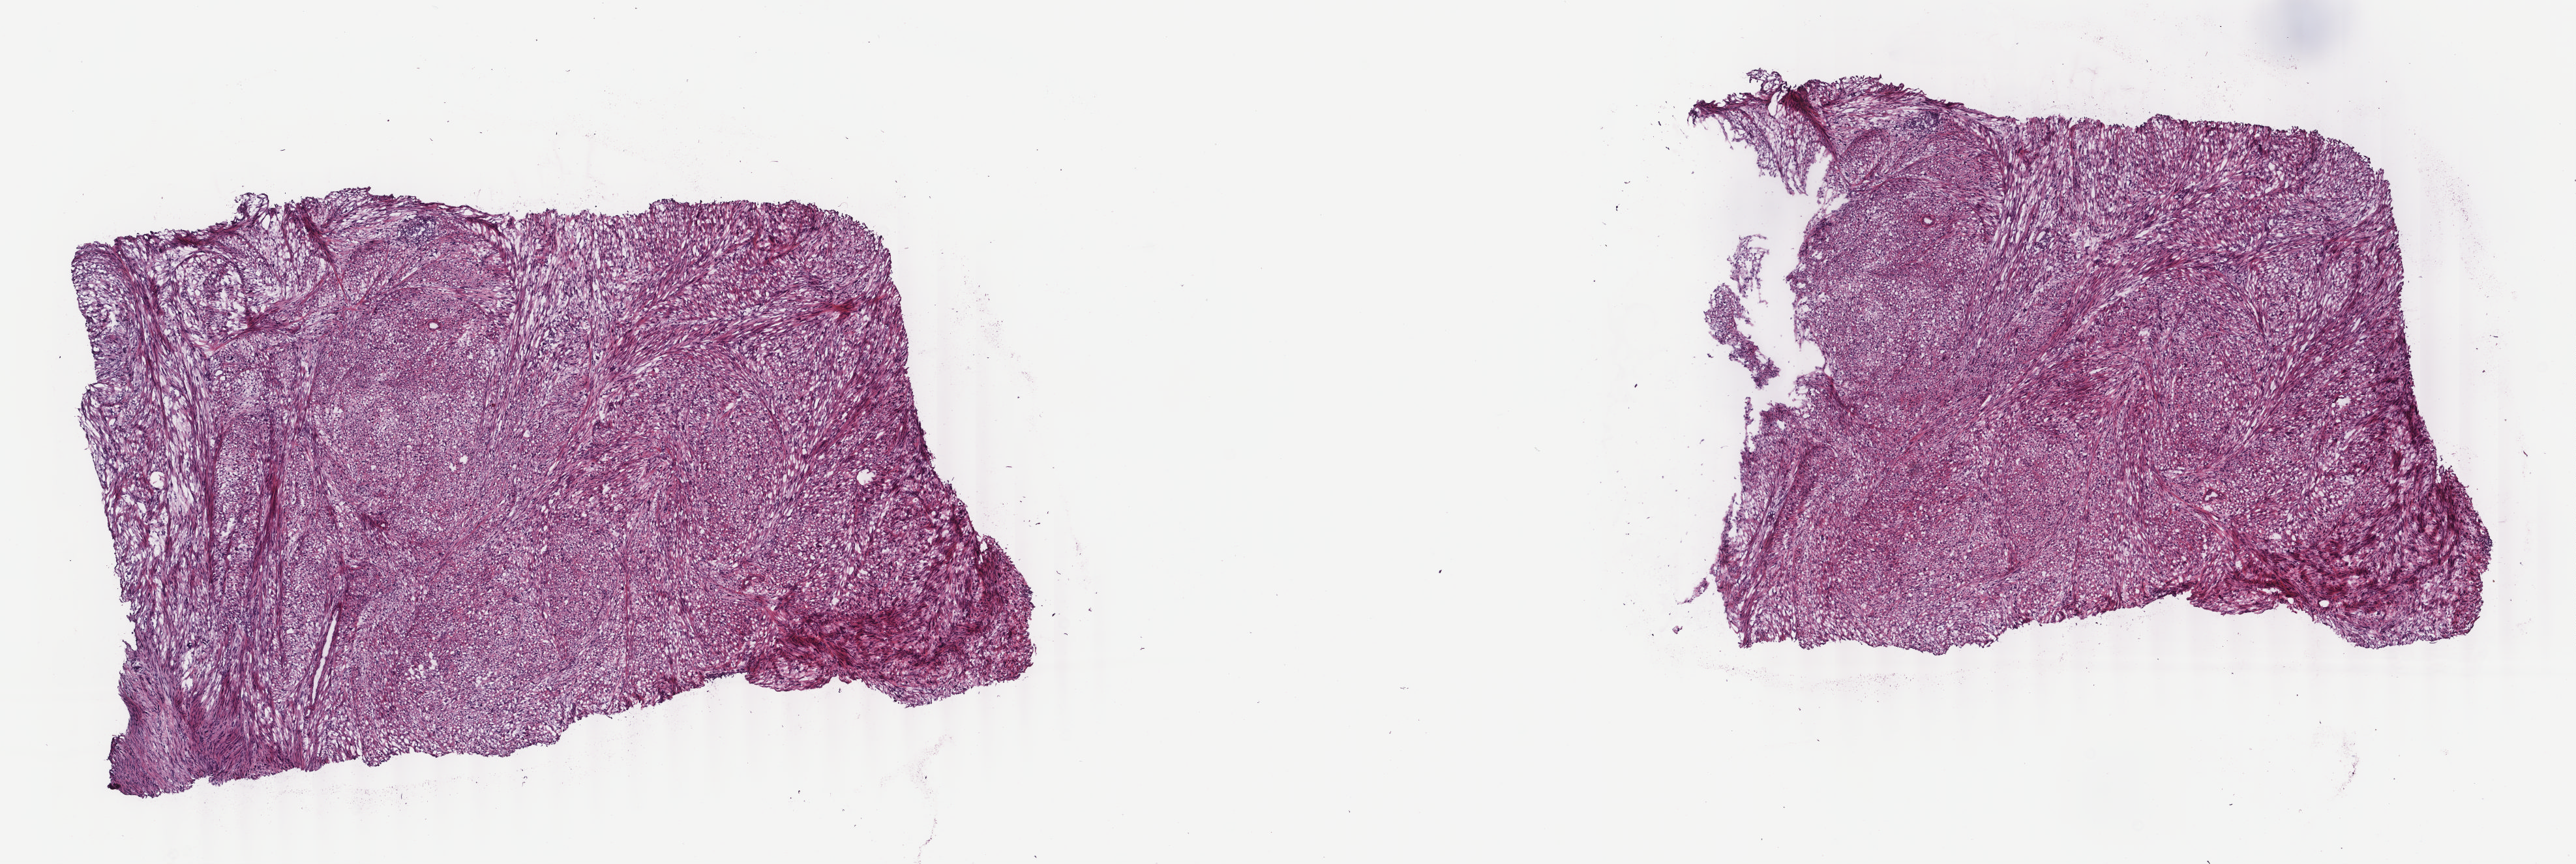
Hematoxylin and eosin (H&E) stained whole-slide image — whole scanned area (about 15.7 x 5.3 mm, acquisition: 40x scan) shown as a low-resolution overview. Frozen section from the top of the tissue portion. Retroperitoneum and peritoneum, primary tumour sample. Patient: male, age at initial diagnosis 74 years. Composition of this section per pathologist review: tumour cells 40%, tumour nuclei 99%, normal cells 0%, stromal cells 59%, necrosis 1%. Infiltration values recorded for this section: lymphocyte infiltration 0%, monocyte infiltration 1%, neutrophil infiltration 0%.
• diagnosis: Dedifferentiated liposarcoma (retroperitoneum)